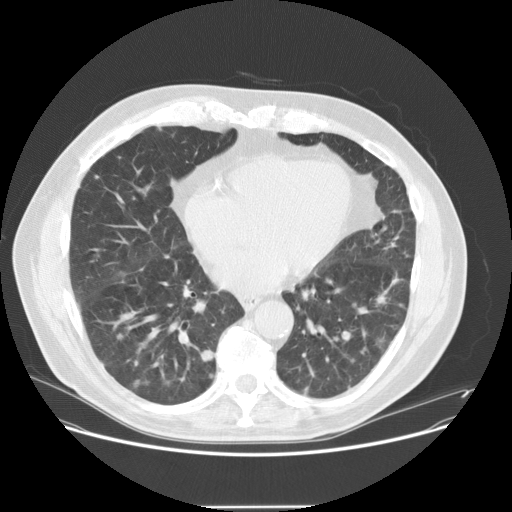
Low-dose screening chest CT, one axial slice; slice 59 of 143 in the series (ordered by position); reconstruction kernel STANDARD; 120 kVp; lung window (W 1500 / L -600 HU); 512 × 512 image matrix.
Structures marked on this image (outlined manually by an expert reader):
- lesion 1 (tumor, lower lobe of right lung): bounding box <202,349,215,362> (left, top, right, bottom; pixels)